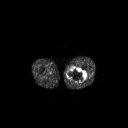
FDG PET of an extremity soft-tissue mass (from a PET/CT study), one axial slice; position 236 of 267 along the scan axis; 3.27 mm slice thickness; 128 × 128 image matrix. Male patient, age 44 years. Case-level facts recorded for this patient, not image findings: histological type: undifferentiated pleomorphic liposarcoma; grade: high; site of the primary tumour: left thigh.
Annotated regions visible in this slice (expert contour drawn on MRI and transferred to this co-registered scan by the dataset authors):
- gross tumour volume including surrounding oedema: box from (x=67, y=68) to (x=86, y=83) px
- gross tumour volume (mass): (x=67, y=68)–(x=86, y=83)